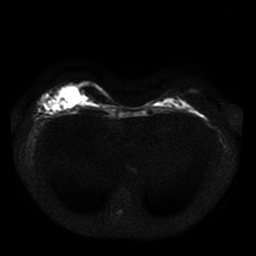
Breast MRI, one axial slice; slice 12 of 41 in the series (ordered by position); diffusion-weighted series; image 2 of 4 stored at this slice position (different b-values; order by instance number); 1.5 T; 256 × 256 image matrix, field of view 330 × 330 mm. Female patient.
Structures marked on this image (outlined manually by an expert reader):
- tumour on diffusion-weighted imaging: box from (x=46, y=99) to (x=65, y=111) px